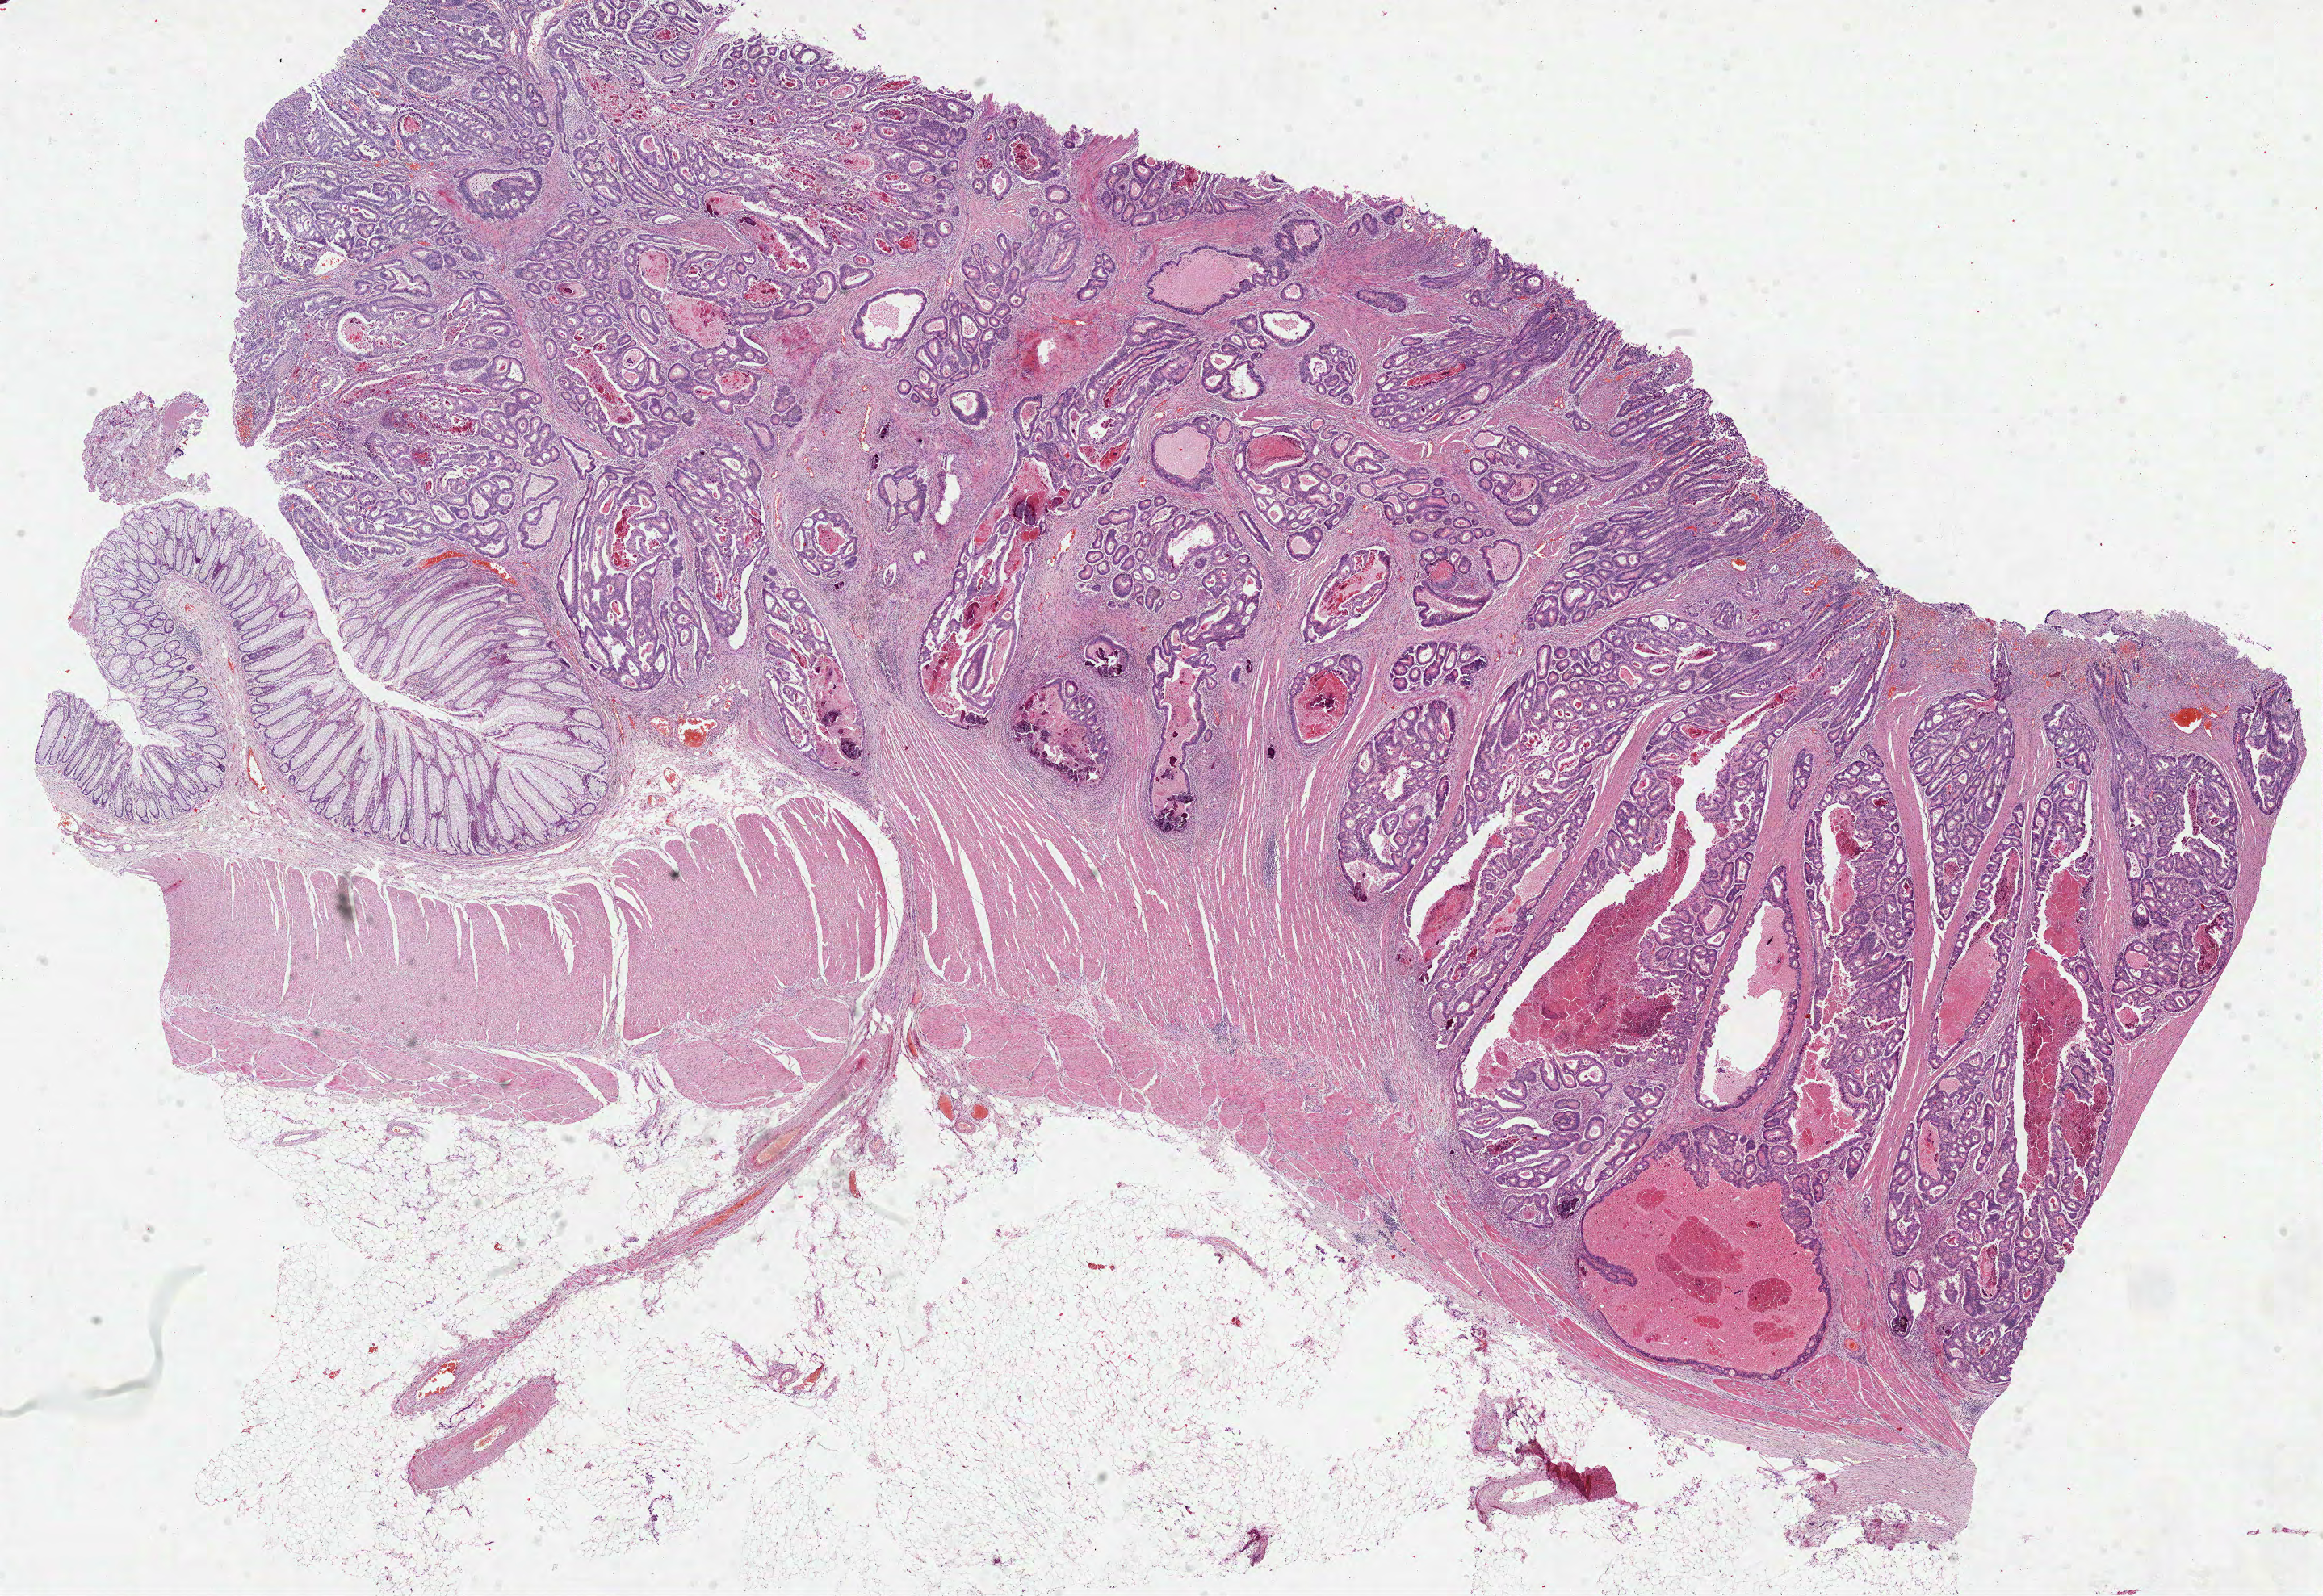
Hematoxylin and eosin (H&E) stained whole-slide image — whole scanned area (about 23.2 x 15.9 mm, acquisition: 40x scan) shown as a low-resolution overview. Formalin-fixed paraffin-embedded (FFPE) diagnostic section. Sample: primary tumour, rectum. Female patient; age at initial diagnosis 59 years.
TNM: T3 N0 M0. Lymph nodes positive (case pathology): 0 of 8 examined. AJCC pathologic stage: IIA. Pathologic diagnosis: Adenocarcinoma in tubulovillous adenoma.